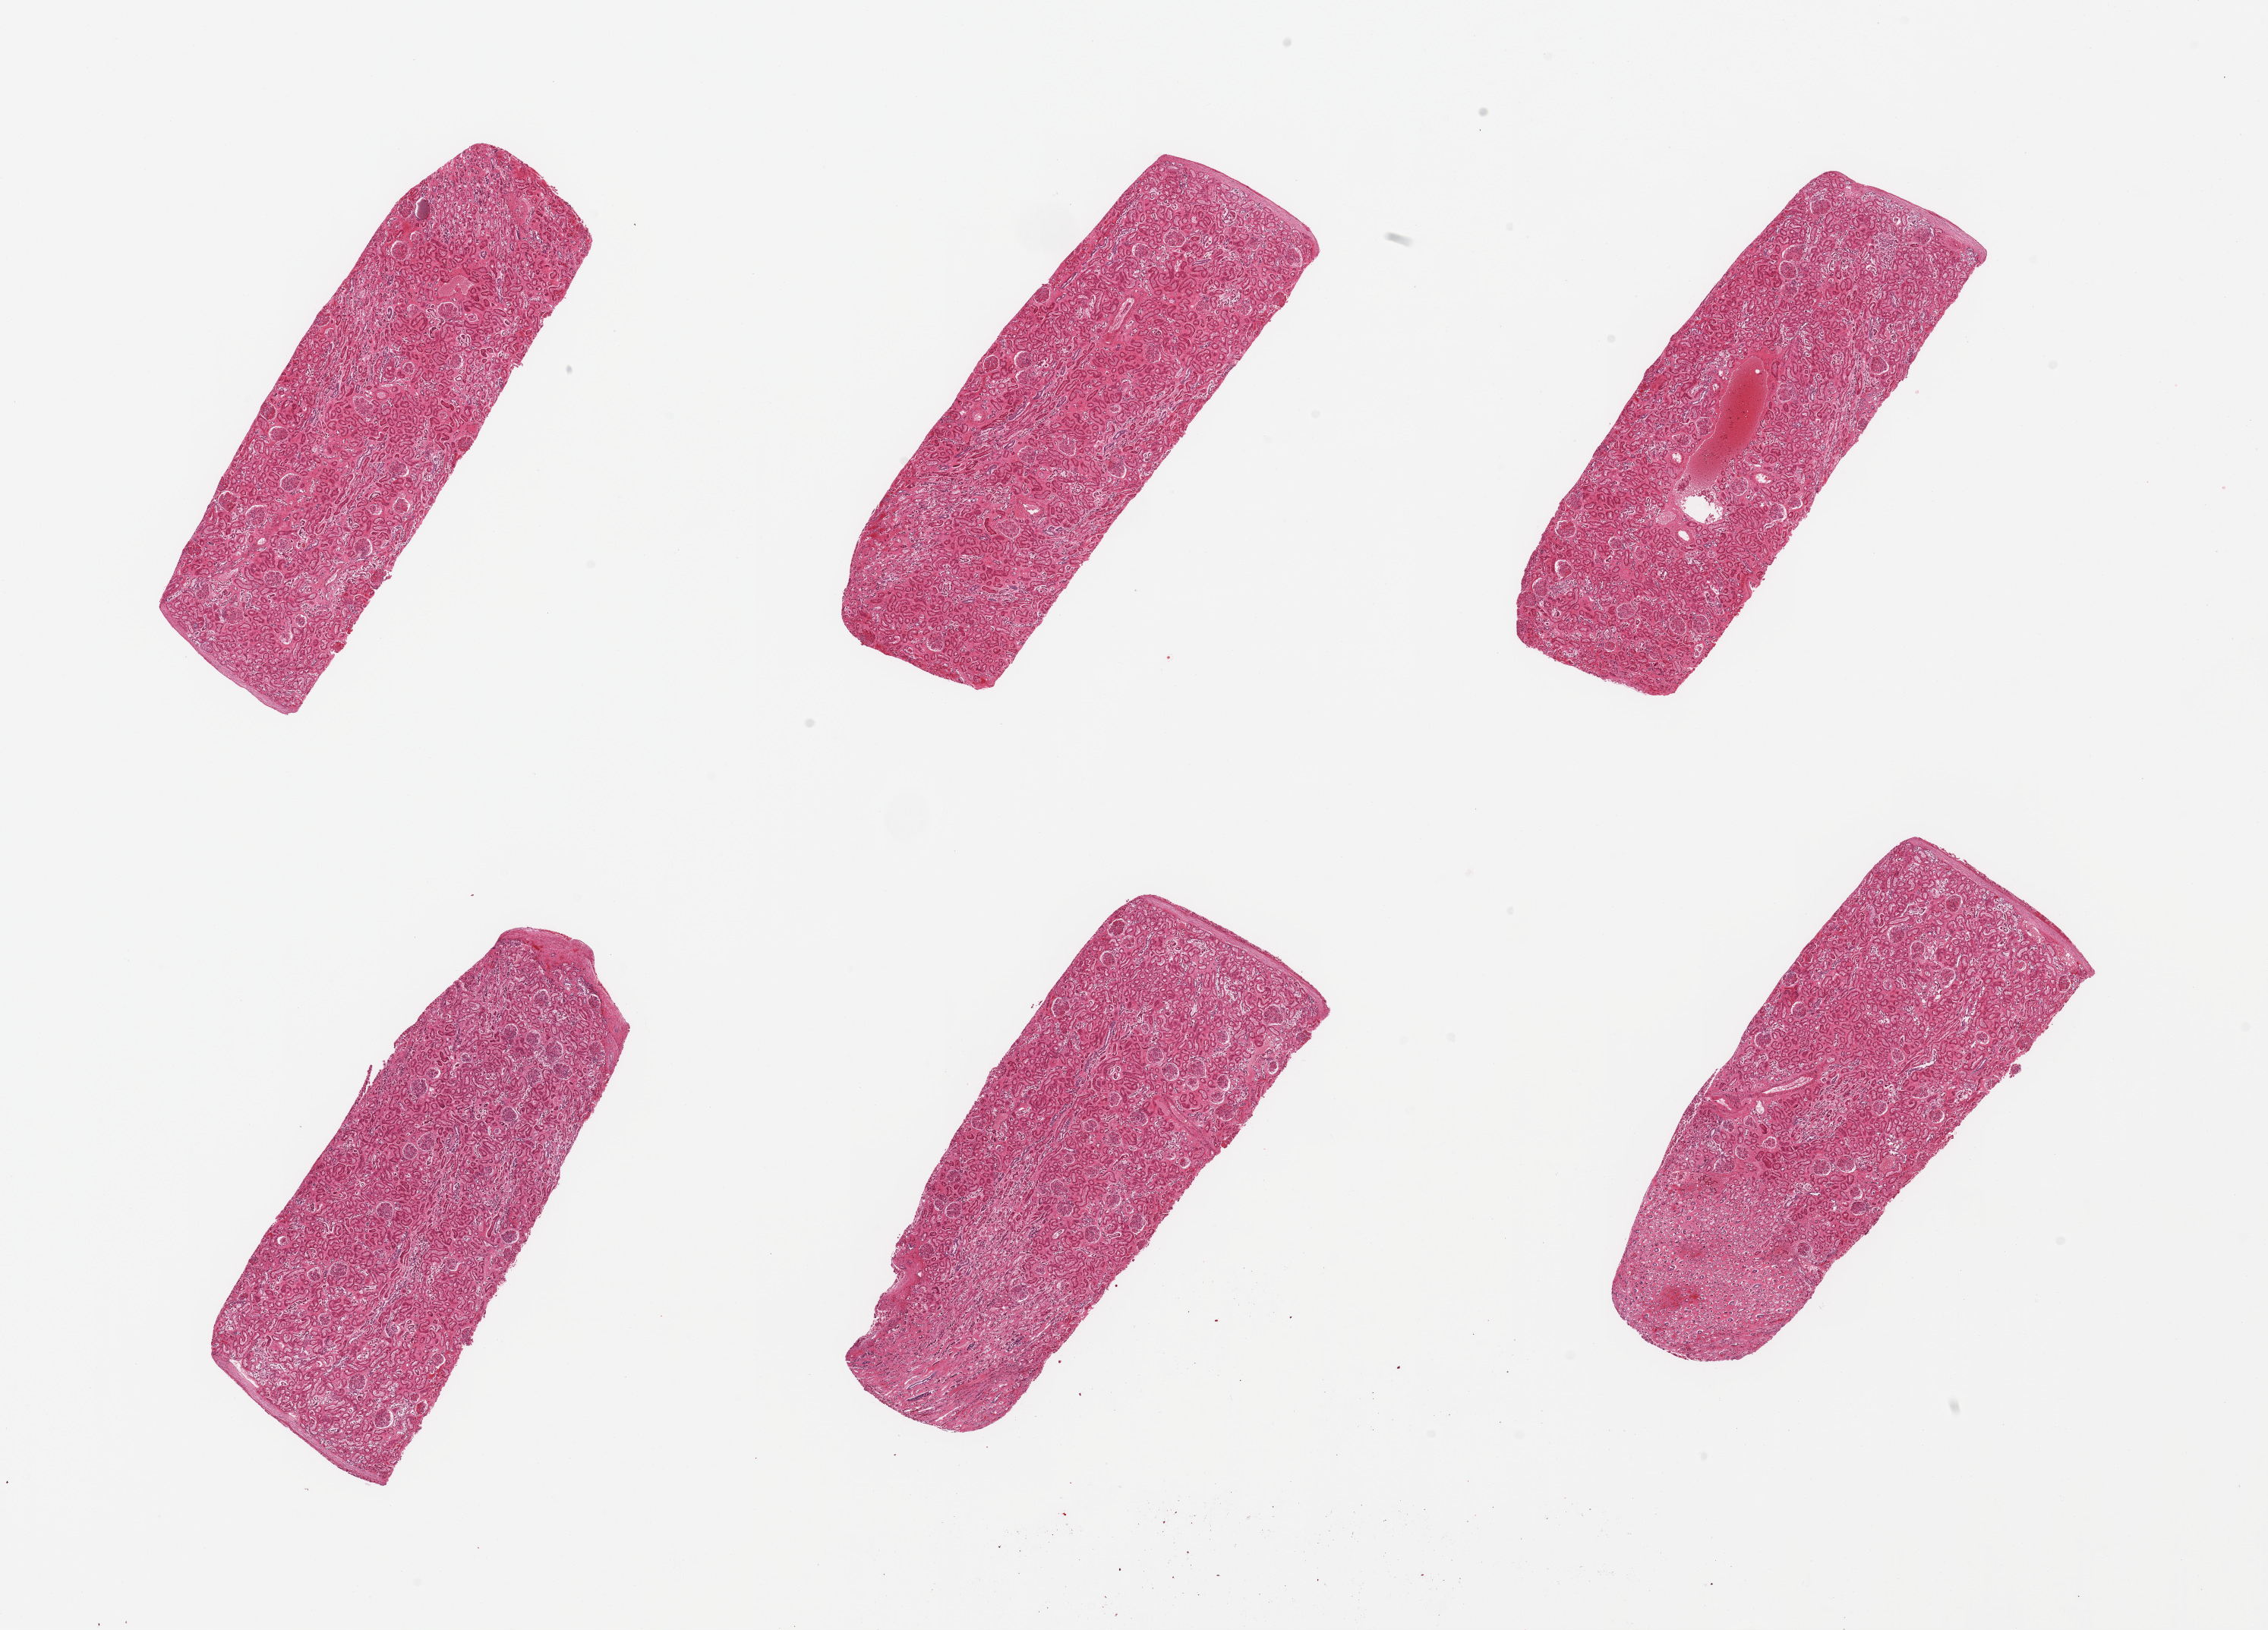
Whole-slide image, haematoxylin and eosin stain, brightfield, a low-resolution overview of the entire scanned area, about 23.6 x 17.0 mm, PAXgene-fixed, paraffin-embedded tissue, target tissue: renal cortex, tissue donor sample. Donor: male.
* reviewer comment on this tissue sample: 6 pieces, moderately advanced tubular autolysis